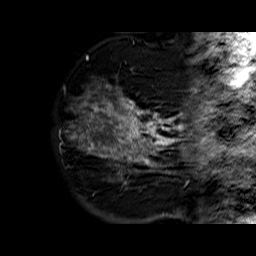
Breast MRI (dynamic contrast-enhanced), one sagittal slice. Position 14 of 60 along the scan axis. Dynamic contrast-enhanced series, time point 2 of 6 at this slice position (early post-contrast). 1.5 T. TE 6.3 ms, TR 32.4 ms. 4 mm slice thickness. 256 × 256 image matrix, field of view 200 × 200 mm. Female patient. Case-level facts recorded for this patient, not image findings: setting: breast cancer imaged before/during neoadjuvant chemotherapy; receptor status: HR-positive, HER2-negative.
Outlined on this slice (semi-automatic segmentation, software-assisted and operator-edited):
- analysis volume of interest (the breast-tissue region the enhancement analysis was run in; not a lesion): box from (x=71, y=81) to (x=177, y=183) px
- tumour enhancement mask (voxels above the 100 % enhancement threshold inside the analysis volume of interest): (x=80, y=84)–(x=177, y=183)